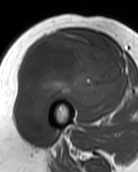
MRI of an extremity soft-tissue mass, one axial slice. Slice 55 of 99 in the series (ordered by position). MR volume resampled by the dataset authors to the PET/CT grid (not the native acquisition matrix). 3.27 mm slice thickness. 138 × 172 image matrix, field of view 135 × 168 mm. Female patient. From the clinical record (not read from this slice): histological type: pleiomorphic undifferentiated sarcoma; grade: high; site of the primary tumour: right quadricep.
Outlined on this slice (expert contour drawn on MRI and transferred to this co-registered scan by the dataset authors):
- gross tumour volume including surrounding oedema: bounding box (x1, y1, x2, y2) in pixels: (16, 32, 123, 138)
- gross tumour volume (mass): (16, 32, 123, 138)